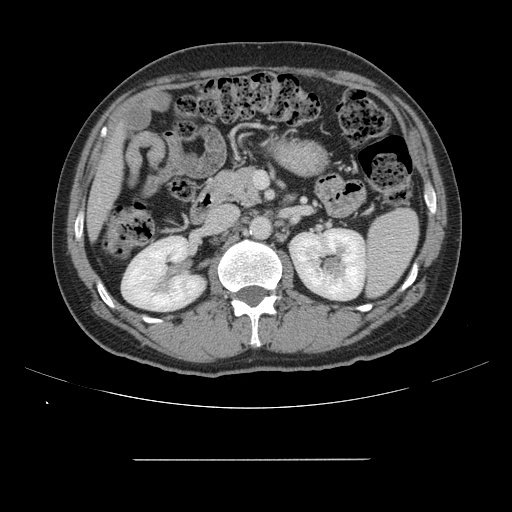
Contrast-enhanced abdominal CT, one axial slice. Slice 62 of 164 in the series (ordered by position). Soft-tissue window (W 400 / L 40 HU). 2.5 mm slice thickness. 512 × 512 image matrix, field of view 404 × 404 mm. Male patient, age 54 years. Case-level facts recorded for this patient, not image findings: diagnosis: colorectal cancer liver metastases, imaged before liver resection; multiple liver metastases: yes.
Outlined on this slice (outlined manually by an expert reader):
- liver: bounding box <88,130,123,235> (left, top, right, bottom; pixels)
- planned liver remnant (the part of the liver to remain after resection): <88,132,122,235>